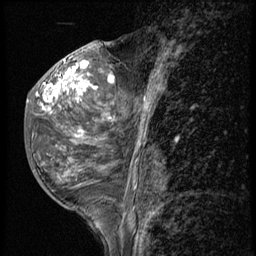
Breast MRI (dynamic contrast-enhanced), one sagittal slice. Slice 23 of 56 in the series (ordered by position). 3 images stored at this slice position (order not interpretable as contrast timing). 1.5 T. TE 4.2 ms, TR 9 ms. 2.5 mm slice thickness. 256 × 256 image matrix, field of view 180 × 180 mm. Female patient, age 50 years. Case-level facts recorded for this patient, not image findings: setting: breast cancer imaged before/during neoadjuvant chemotherapy; receptor status: triple-negative.
Annotated regions visible in this slice (semi-automatic segmentation, software-assisted and operator-edited):
- analysis volume of interest (the breast-tissue region the enhancement analysis was run in; not a lesion): box from (x=25, y=50) to (x=117, y=191) px
- tumour enhancement mask (voxels above the 140 % enhancement threshold inside the analysis volume of interest): (x=42, y=61)–(x=113, y=135)